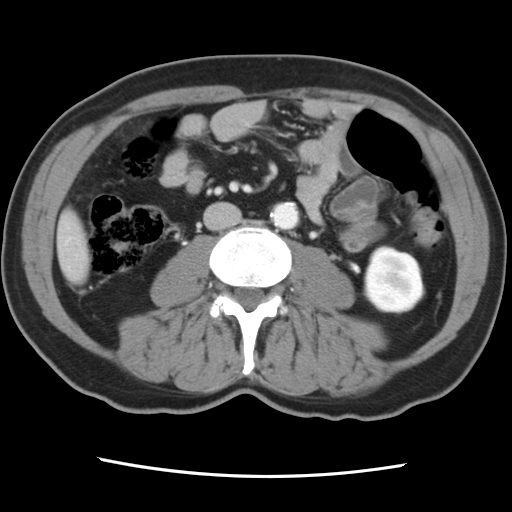
Contrast-enhanced abdominal CT, one axial slice. Position 15 of 83 along the scan axis. 120 kVp. Intravenous contrast given. Soft-tissue window (W 400 / L 40 HU). 5 mm slice thickness. 512 × 512 image matrix, field of view 321 × 321 mm. Male patient, age 69 years. Case-level facts recorded for this patient, not image findings: diagnosis: colorectal cancer liver metastases, imaged before liver resection; multiple liver metastases: yes; largest metastasis: 3.5 cm.
Annotated regions visible in this slice (manually delineated by an expert):
- liver: box from (x=59, y=214) to (x=89, y=282) px
- planned liver remnant (the part of the liver to remain after resection): (x=59, y=213)–(x=89, y=281)